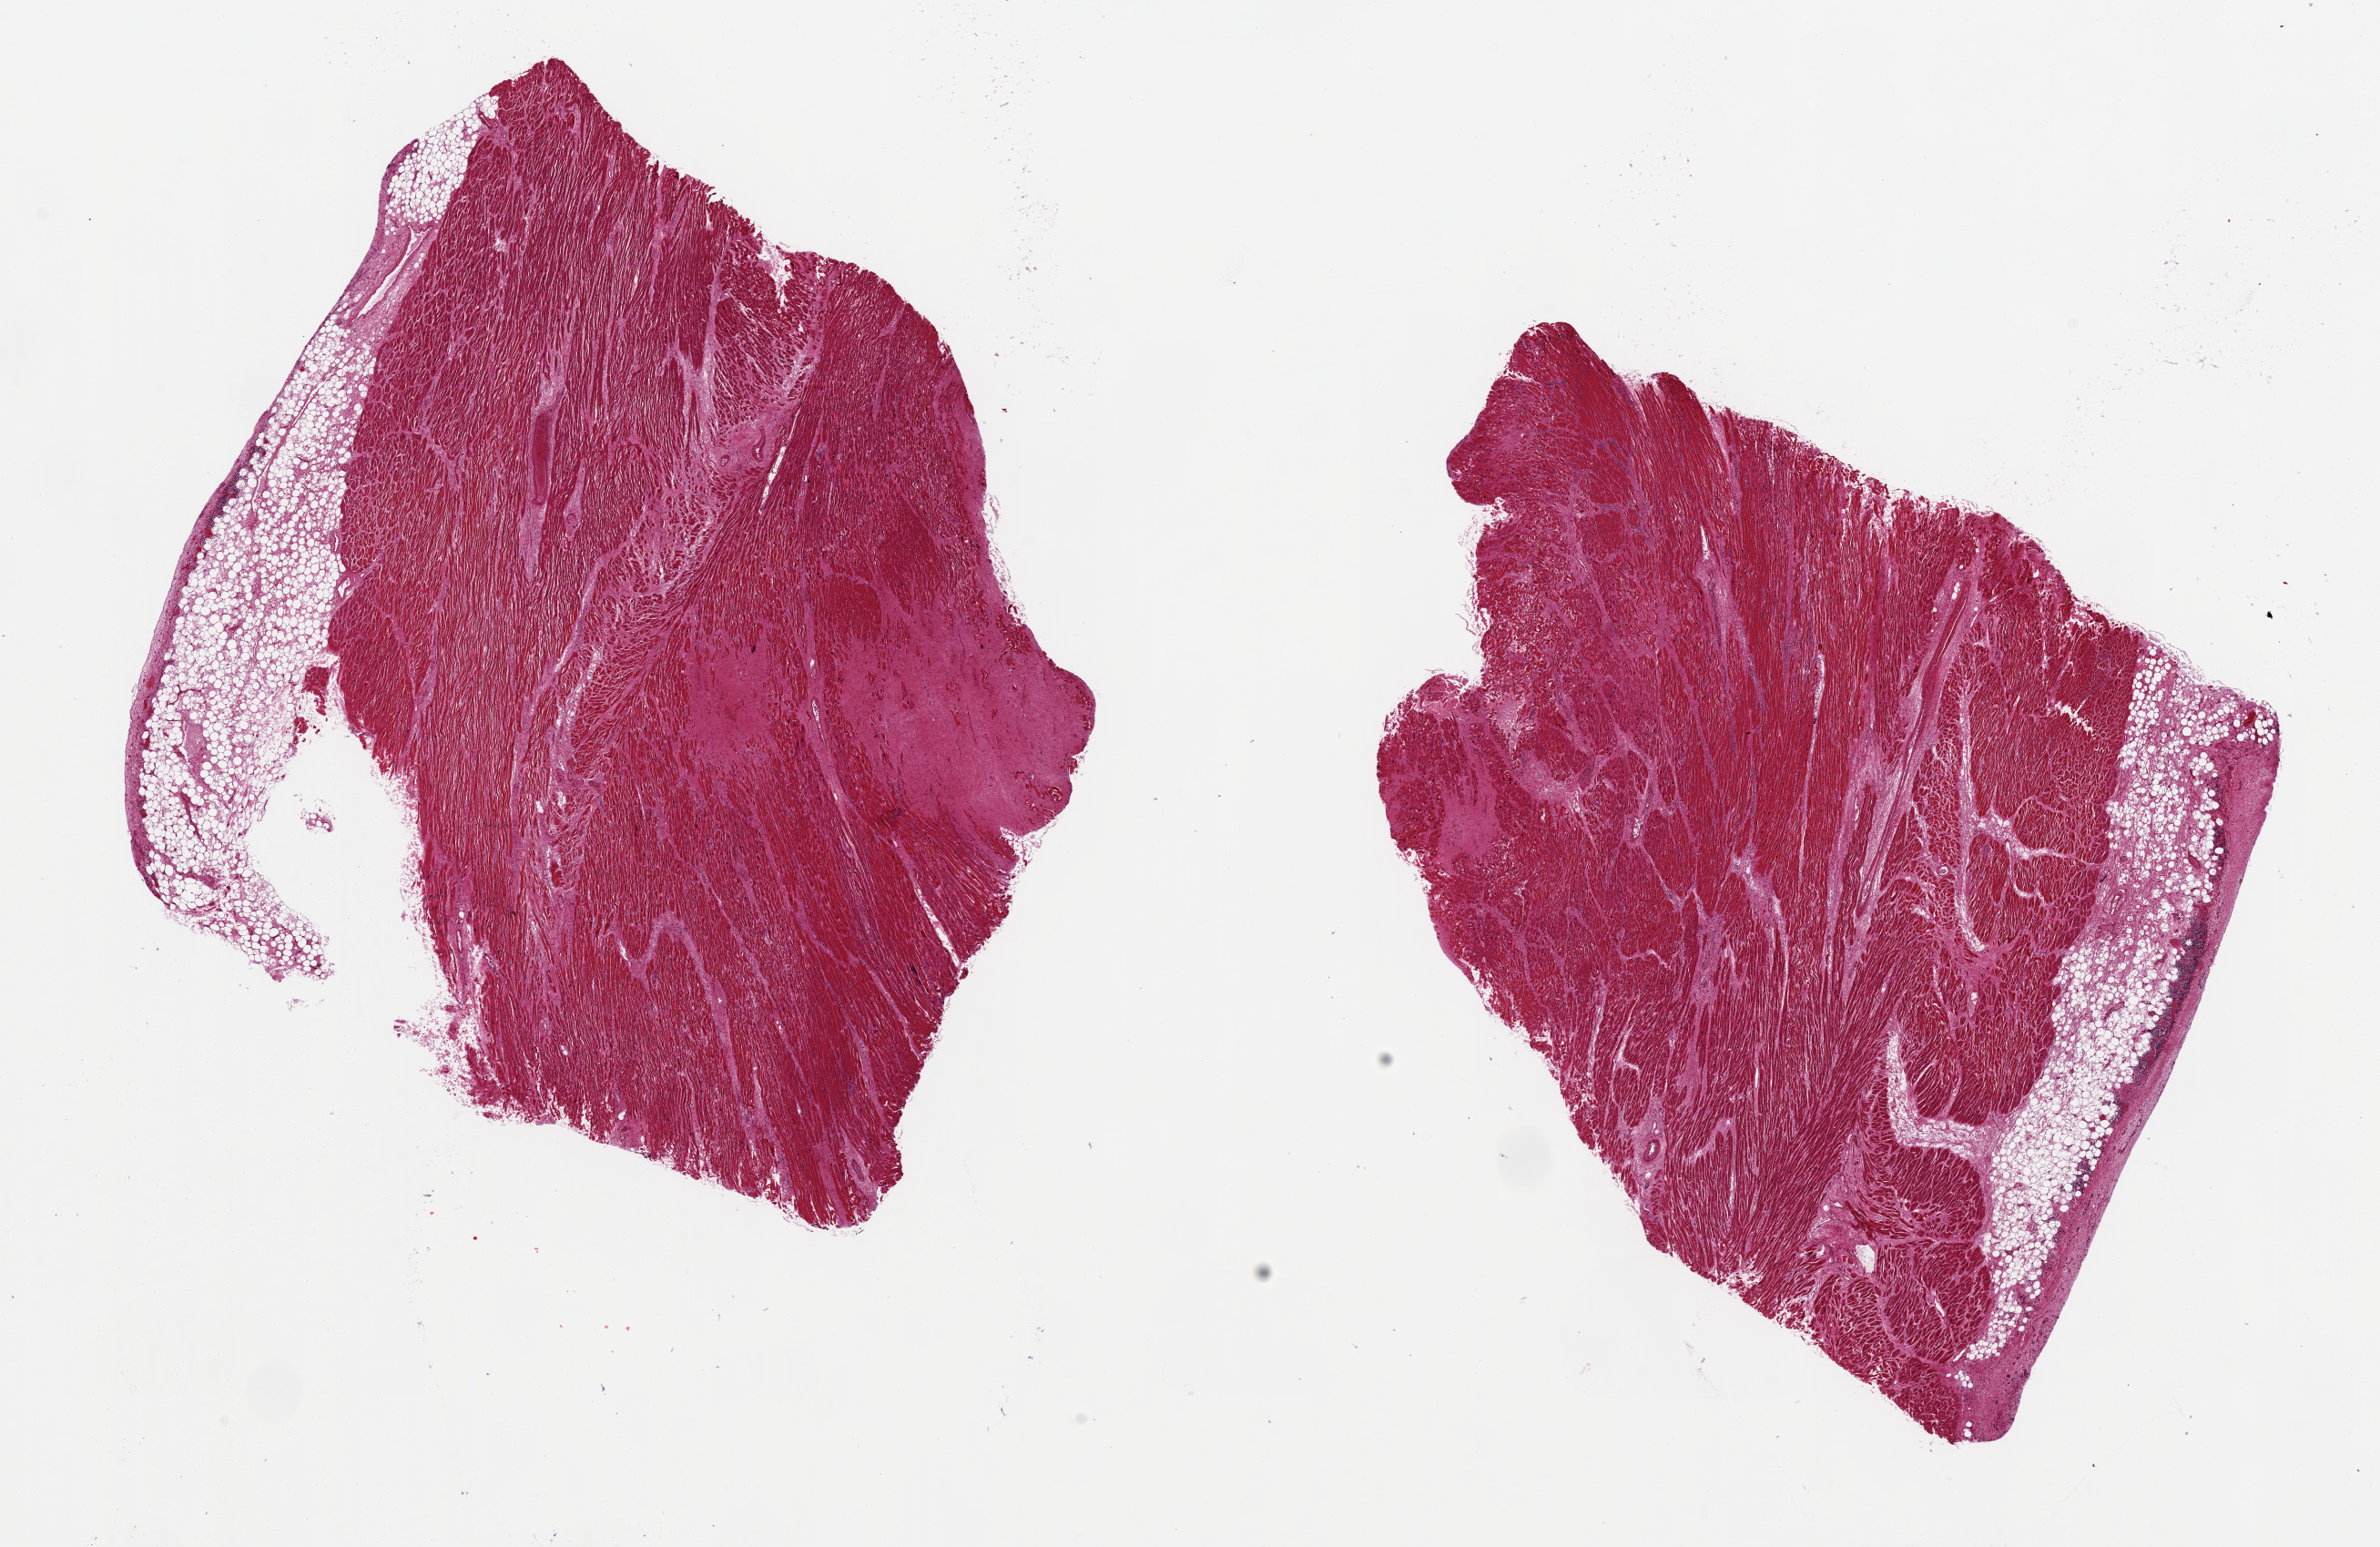
Digitized haematoxylin and eosin-stained section, brightfield — low-resolution overview of the scanned area, about 20.7 x 13.4 mm (from a 20x scan), PAXgene-fixed, paraffin-embedded tissue, target tissue: heart, tissue donor sample. Male donor.
Pathologist's review note for this sample: 2 aliquots, ~8x8mm. Patchy confluient healed infarcts up to ~3.5mm d. Ischemic changes diffusely.